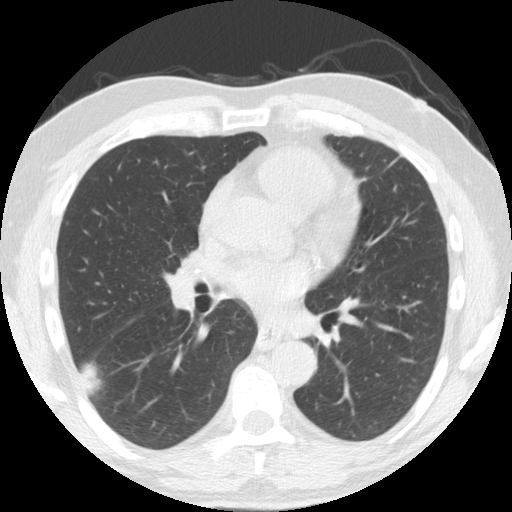
Axial slice from a low-dose chest CT screening exam, second annual screen, lung window (W 1500 / L -600 HU), slice 88 of 174 in the series. Male, age 61 years at enrolment. Former smoker at enrolment.
Lesion marked by an expert reader, bounding box [x1, y1, x2, y2] px = [54, 329, 121, 403]. Reader record for this screening exam (exam-level; its link to the box is not recorded): non-calcified nodule or mass ≥4 mm, right lower lobe, 33 × 19 mm, smooth margins, soft tissue attenuation, pre-existing on the prior screen: yes; interval growth: yes.